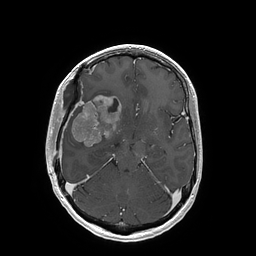
Brain MRI from a brain-tumour surgery series, one axial slice; slice 104 of 202 in the series (ordered by position); T1-weighted post-contrast; 256 × 256 image matrix, field of view 250 × 250 mm. Case-level facts recorded for this patient, not image findings: histopathology: Glioblastoma; WHO grade: 4; IDH mutation: no; tumour location: Right Insular.
Structures marked on this image (outlined manually by an expert reader):
- tumour: box from (x=71, y=95) to (x=121, y=147) px